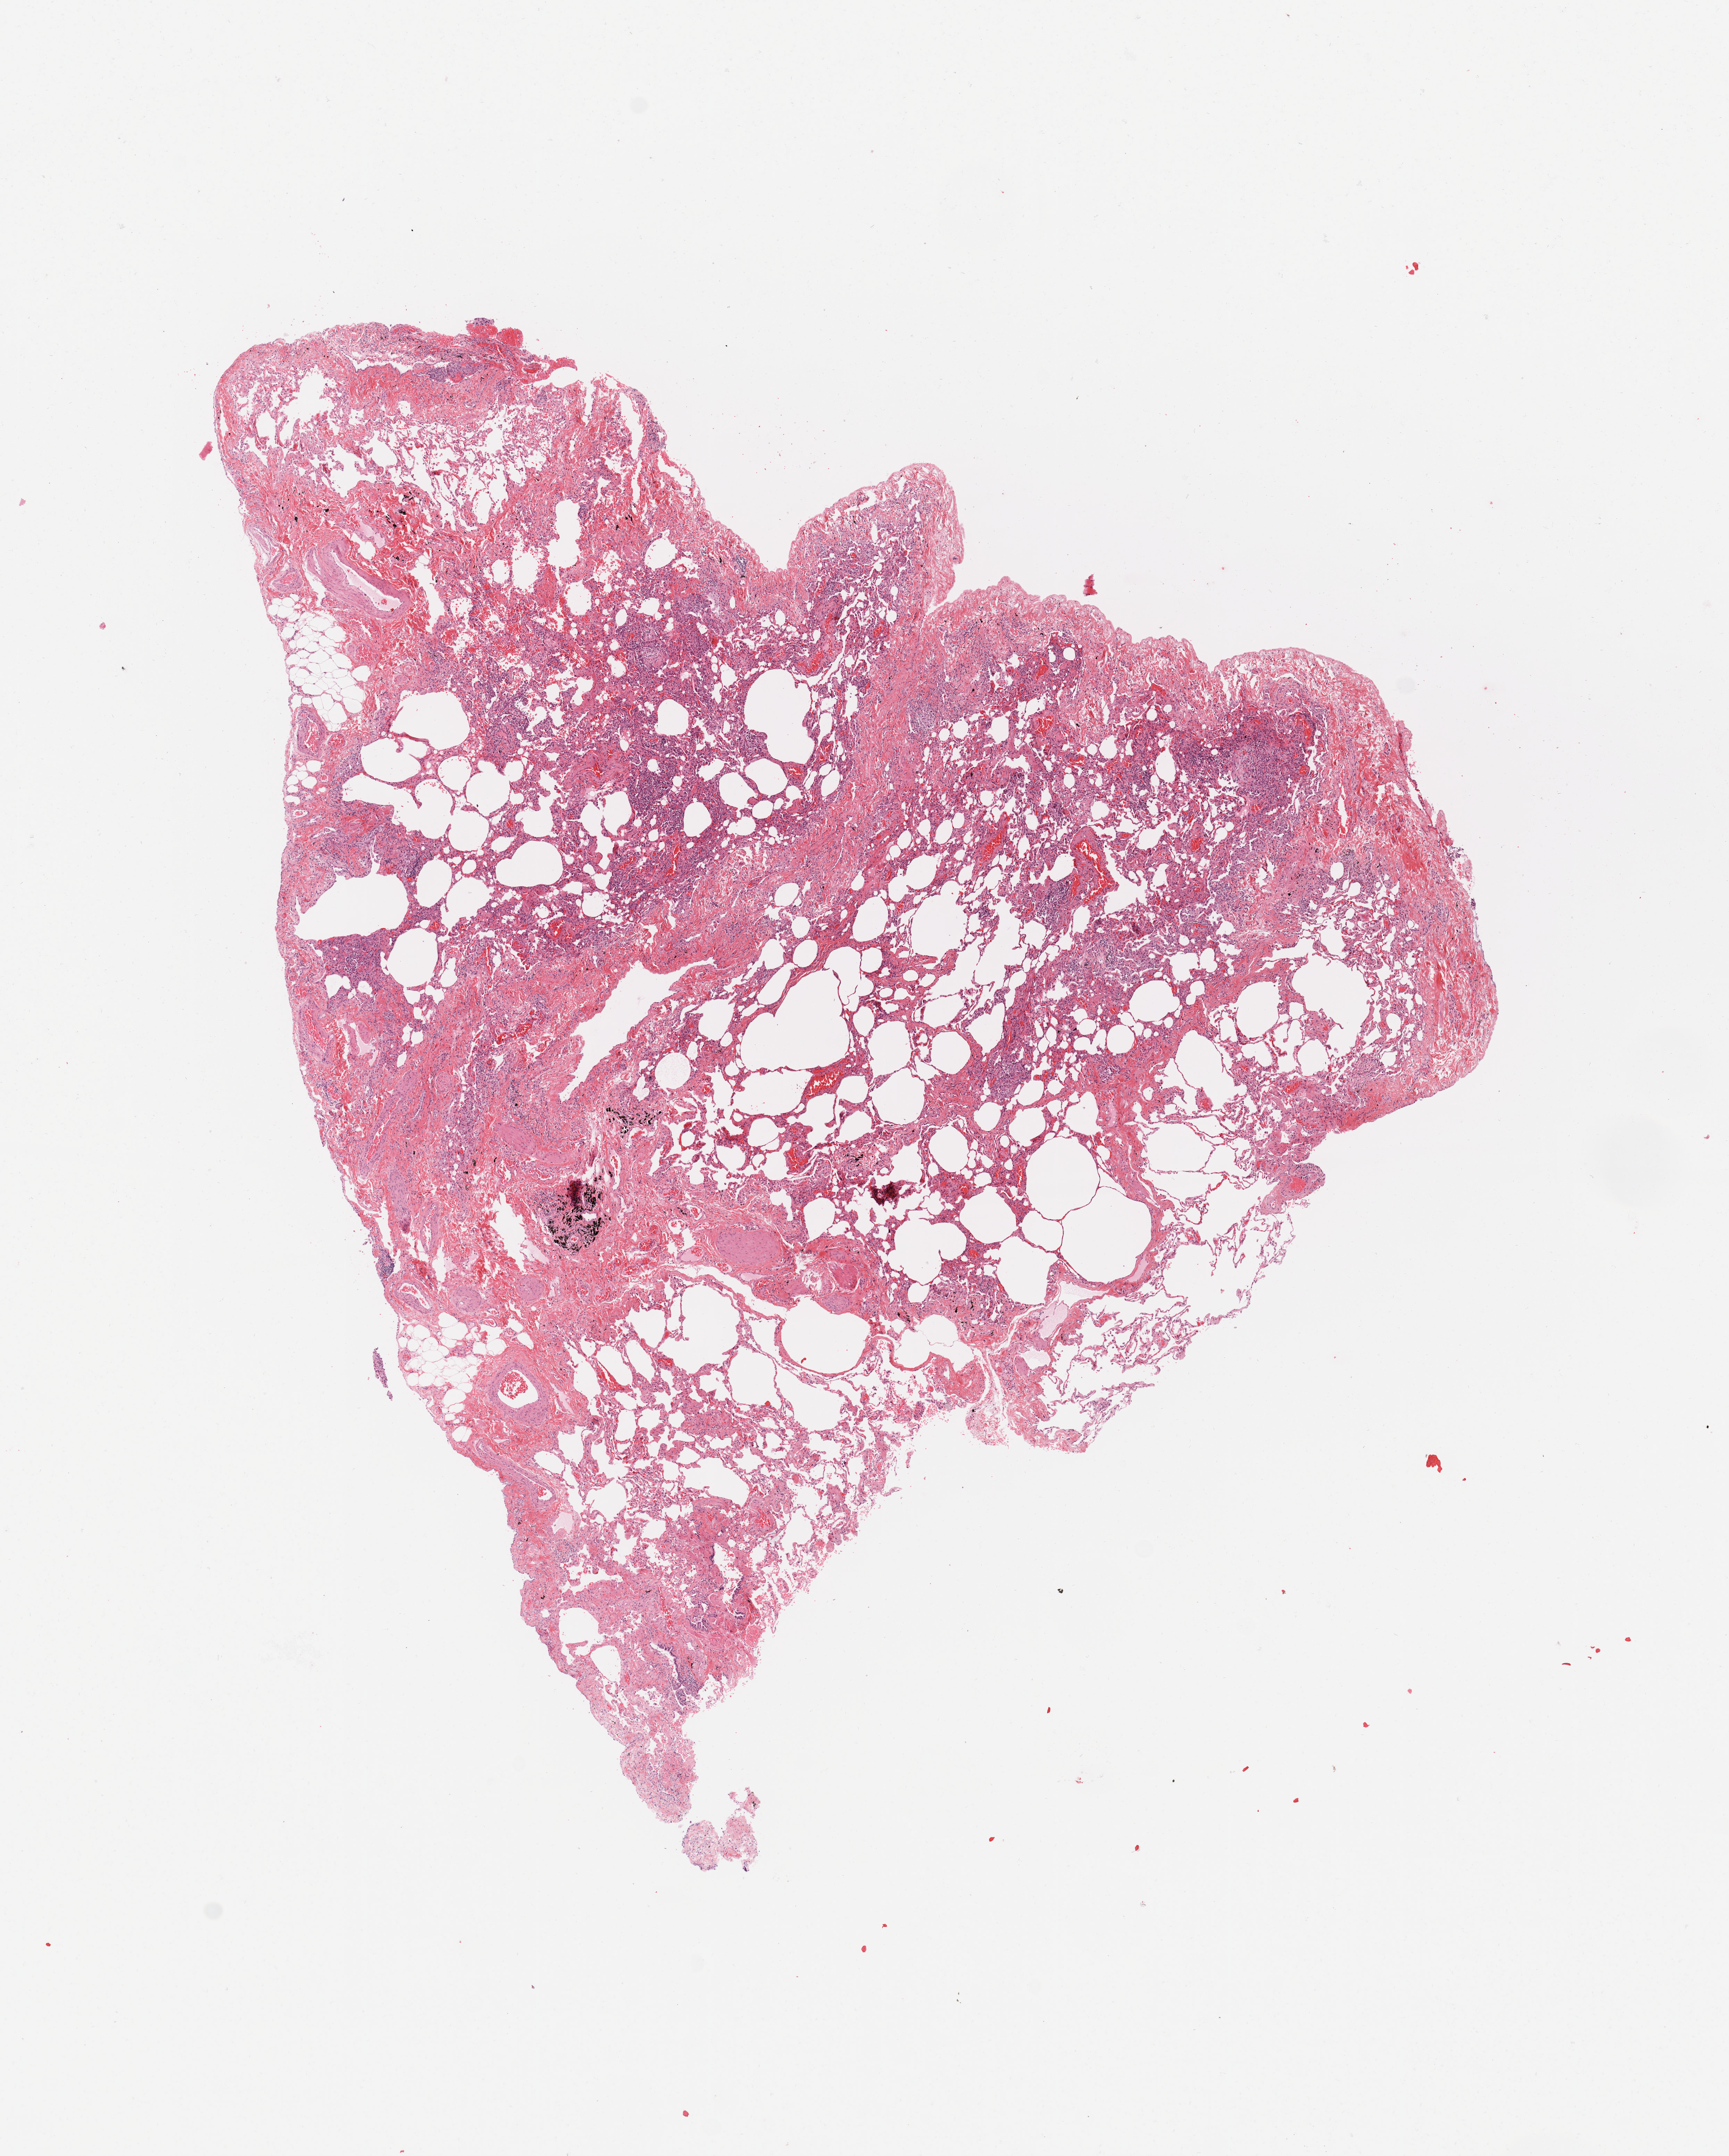
Hematoxylin and eosin (H&E) stained whole-slide image, low-resolution overview of the scanned area, about 9.8 x 12.3 mm (acquisition: 20x scan). Normal (non-tumour) tissue sample, sampled site: lung. Male, 77 y/o.
This section: normal (non-tumour) tissue from the same patient. Patient diagnosis: Adenocarcinoma, NOS.